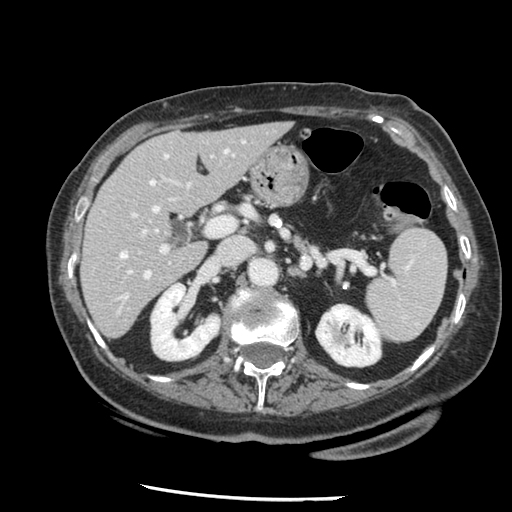
Contrast-enhanced abdominal CT, one axial slice. Position 76 of 148 along the scan axis. Intravenous contrast given. Soft-tissue window (W 400 / L 40 HU). 2.5 mm slice thickness. 512 × 512 image matrix. Female patient, age 85 years. Case-level facts recorded for this patient, not image findings: diagnosis: colorectal cancer liver metastases, imaged before liver resection; multiple liver metastases: no; largest metastasis: 0.9 cm; chemotherapy before resection: yes.
Outlined on this slice (outlined manually by an expert reader):
- hepatic veins: box from (x=120, y=142) to (x=177, y=299) px
- liver: (x=82, y=124)–(x=289, y=337)
- planned liver remnant (the part of the liver to remain after resection): (x=82, y=124)–(x=289, y=337)
- portal vein (with intrahepatic branches): (x=127, y=148)–(x=230, y=274)